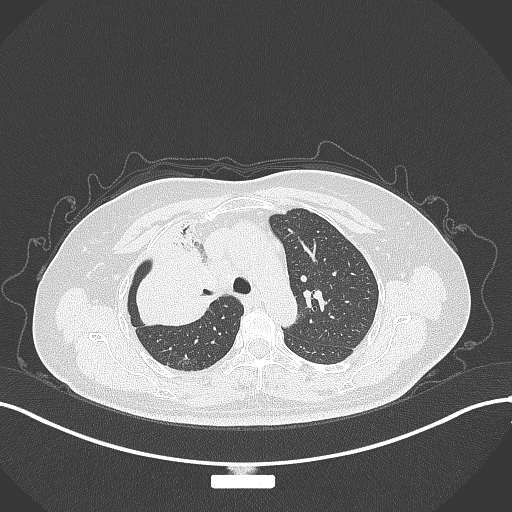
Chest CT, one axial slice; slice 222 of 309 in the series (ordered by position); reconstruction kernel B70f; 120 kVp; lung window (W 1500 / L -600 HU); 1 mm slice thickness; 512 × 512 image matrix. Female patient, age 60 years. From the clinical record (not read from this slice): clinical TNM (as recorded): T3 N1 M1.
Outlined on this slice (bounding box drawn by a radiologist):
- lung tumour (recorded histology: adenocarcinoma): bounding box <126,236,226,334> (left, top, right, bottom; pixels)